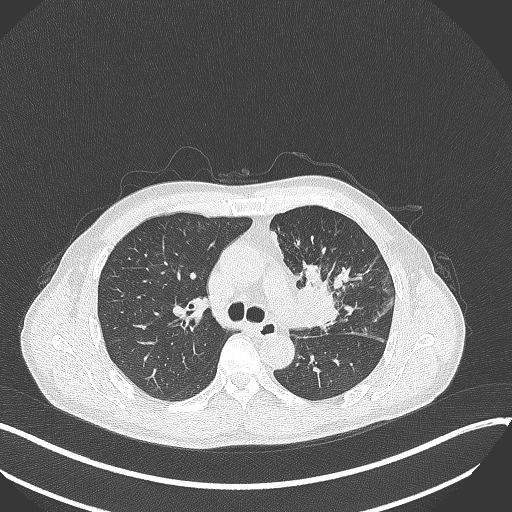
Chest CT, one axial slice; position 221 of 411 along the scan axis; reconstruction kernel B70f; lung window (W 1500 / L -600 HU); 1 mm slice thickness; 512 × 512 image matrix. Male patient, age 56 years. From the clinical record (not read from this slice): clinical TNM (as recorded): T2a N0 M0.
Structures marked on this image (bounding box drawn by a radiologist):
- lung tumour (recorded histology: squamous cell carcinoma): bounding box [x1, y1, x2, y2] px = [290, 262, 342, 334]